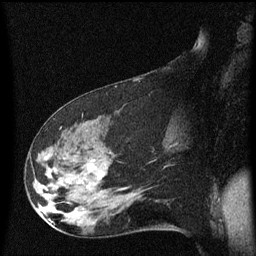
Breast MRI (dynamic contrast-enhanced), one sagittal slice. Position 30 of 60 along the scan axis. Dynamic contrast-enhanced series, image 2 of 3 at this slice position (ordered by acquisition). 1.5 T. TE 4.2 ms, TR 8.4 ms. 256 × 256 image matrix, field of view 200 × 200 mm. Patient: female, 48 years.
Outlined on this slice (semi-automatic segmentation, software-assisted and operator-edited):
- analysis volume of interest (the breast-tissue region the enhancement analysis was run in; not a lesion): box from (x=31, y=120) to (x=134, y=225) px
- tumour enhancement mask (voxels above the 70 % enhancement threshold inside the analysis volume of interest): (x=99, y=174)–(x=104, y=179)